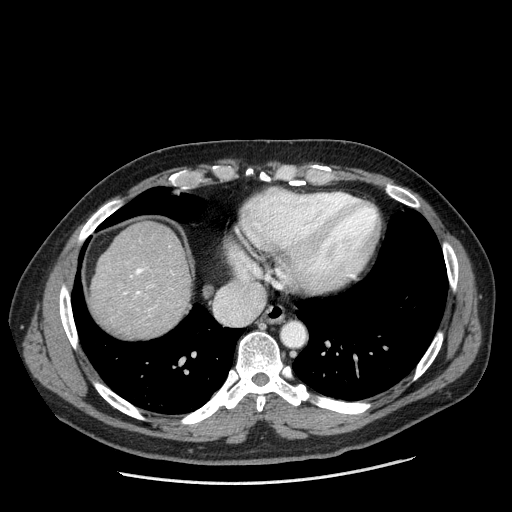
Contrast-enhanced abdominal CT (liver protocol), one axial slice. Position 171 of 198 along the scan axis. Reconstruction kernel STANDARD. One of 2 acquisitions stored at this slice position. Soft-tissue window (W 400 / L 40 HU). 2.5 mm slice thickness. 512 × 512 image matrix, field of view 400 × 400 mm. Case-level facts recorded for this patient, not image findings: diagnosis: hepatocellular carcinoma (patient treated with transarterial chemoembolisation; whether this scan precedes or follows treatment is not stated here); TNM stage (as recorded): Stage-II; Child-Pugh class: A; tumour differentiation: moderately differentiated; tumour nodularity: multinodular.
Annotated regions visible in this slice (semi-automatic segmentation, software-assisted and operator-edited):
- abdominal aorta: bounding box [x1, y1, x2, y2] px = [282, 323, 304, 345]
- liver parenchyma outside the tumour (the mass and vessels are separate outlines, so this box may not span the whole liver): [90, 222, 190, 336]
- liver vessels: [123, 268, 156, 307]